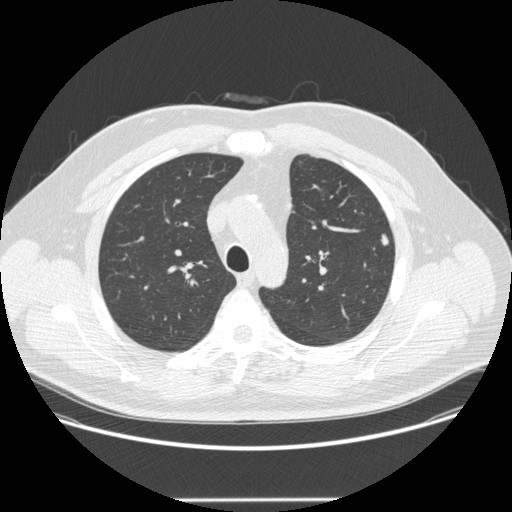
Low-dose screening chest CT, axial slice; baseline annual screen; lung window (W 1500 / L -600 HU); 1.25 mm slice thickness; slice 65 of 252 in the series. Male participant, aged 55 years at enrolment. Former smoker at enrolment.
• Lesion marked by an expert reader, bounding box [x1, y1, x2, y2] px = [373, 230, 402, 257].
• The exam's reader record, not a measurement of the box and not confirmed to be the same lesion: non-calcified nodule or mass ≥4 mm, left upper lobe, 5 × 4 mm, smooth margins, soft tissue attenuation.
• Participant outcome: lung cancer diagnosed 462 days after this screen — adenocarcinoma, NOS, left upper lobe, moderately differentiated (G2), stage IA (AJCC 6th edition), 9 mm at pathology.